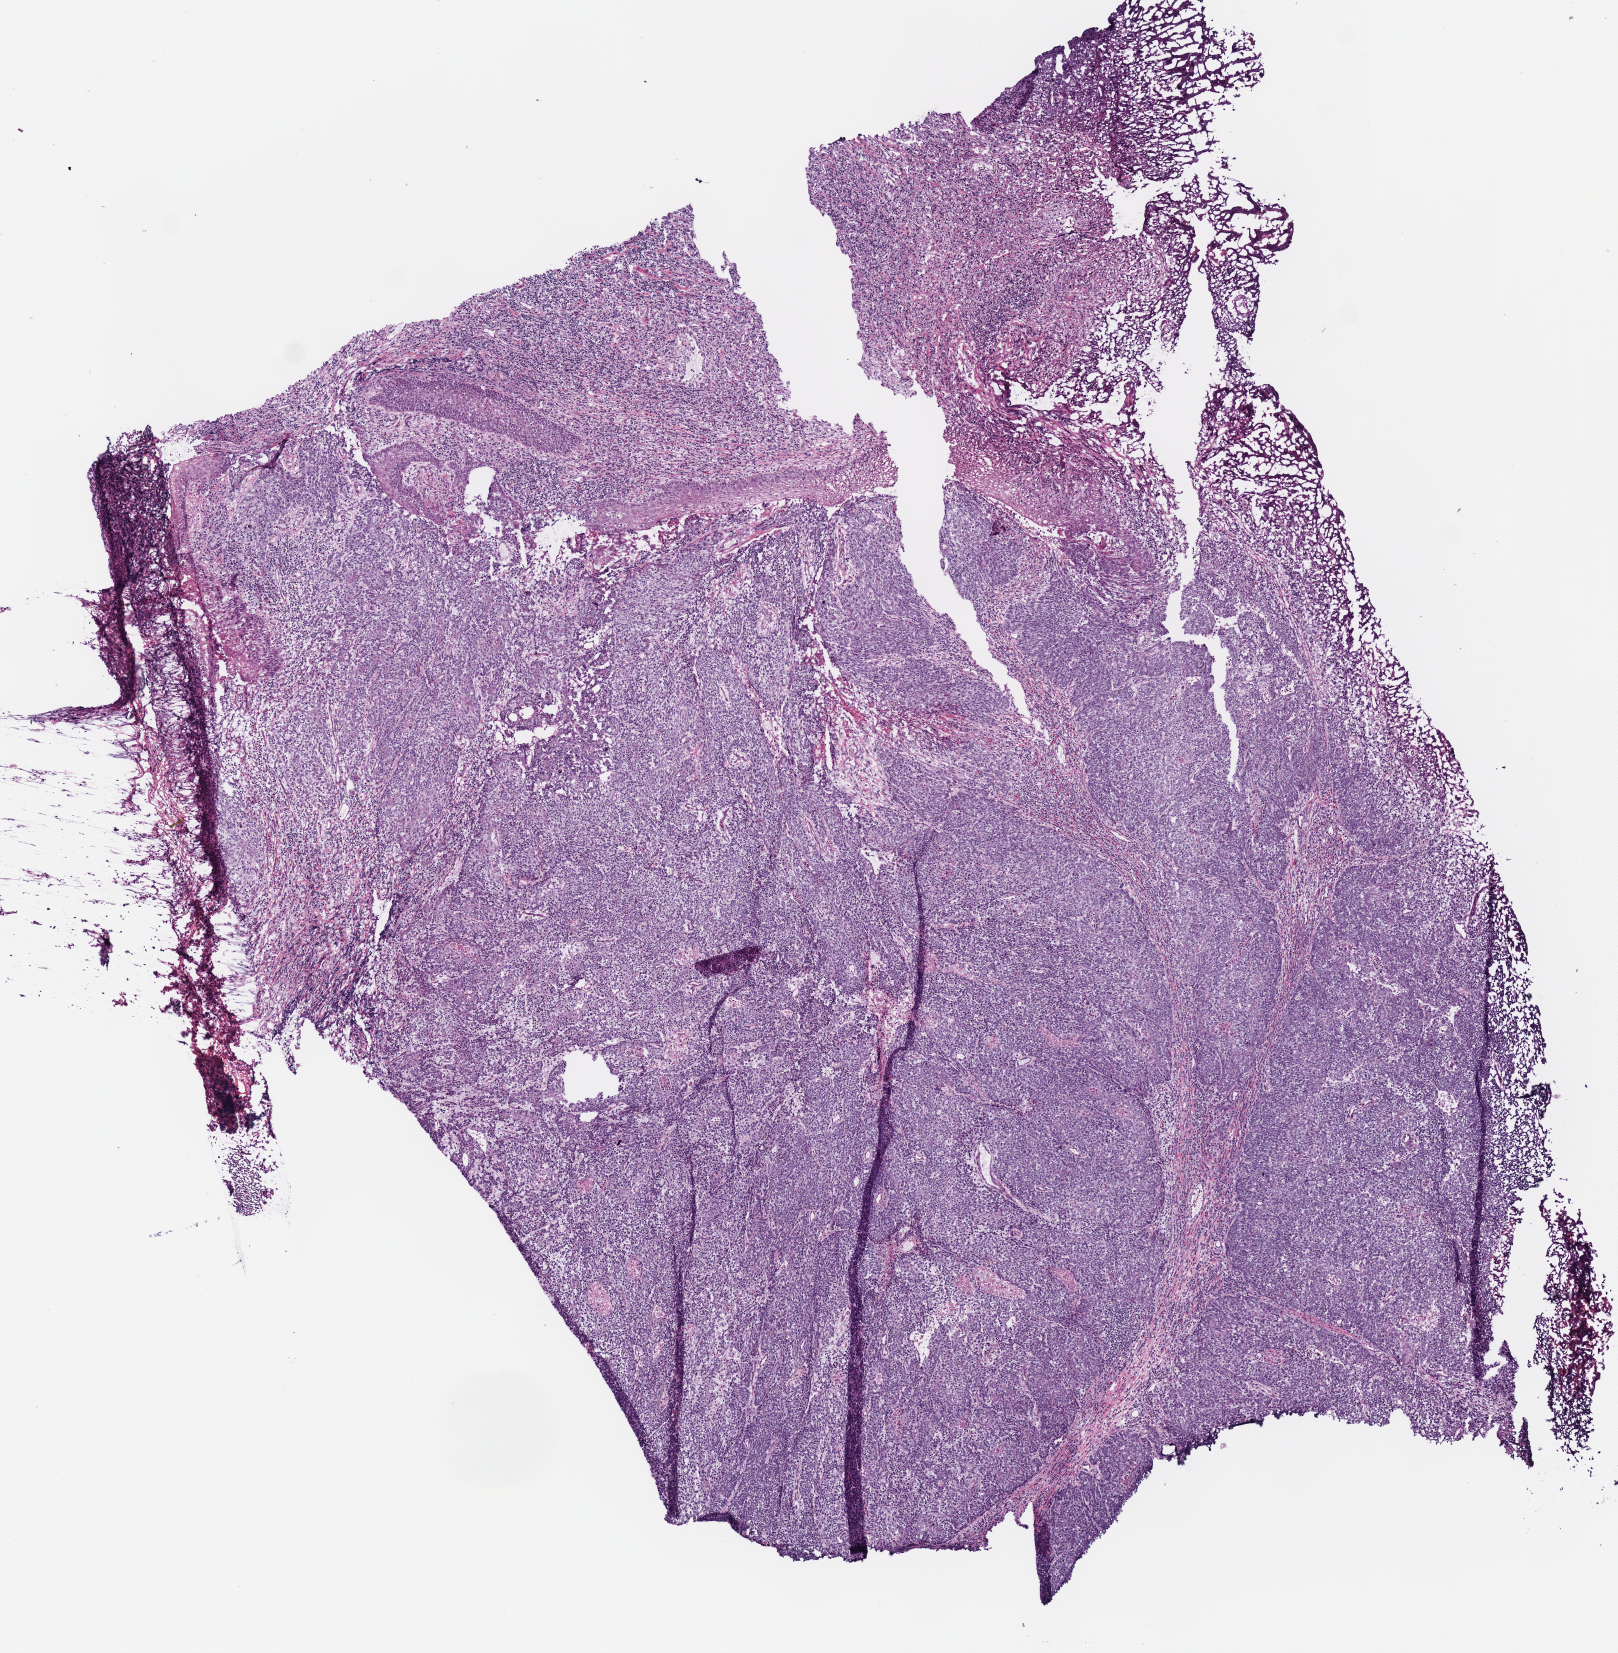
Hematoxylin and eosin (H&E) stained whole-slide image, whole scanned area (about 6.4 x 6.5 mm, from a 40x scan) shown as a low-resolution overview, frozen section from the bottom of the tissue portion, primary tumour sample from the head and neck. Male patient; age at initial diagnosis 40 years. Histologic grade: GX (grade cannot be assessed). Pathologist review of this section (percent, as recorded): tumour cells 92%, tumour nuclei 80%, normal cells 0%, stromal cells 5%, necrosis 3%.
Diagnosis: Squamous cell carcinoma, NOS (tonsil, NOS).